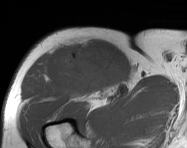
MRI of an extremity soft-tissue mass, one axial slice; position 104 of 114 along the scan axis; MR volume resampled by the dataset authors to the PET/CT grid (not the native acquisition matrix); 3.27 mm slice thickness; 187 × 148 image matrix. Male patient. From the clinical record (not read from this slice): histological type: pleiomorphic leiomyosarcoma; grade: intermediate; site of the primary tumour: right thigh.
Annotated regions visible in this slice (expert contour drawn on MRI and transferred to this co-registered scan by the dataset authors):
- gross tumour volume including surrounding oedema: bounding box <59,40,124,98> (left, top, right, bottom; pixels)
- gross tumour volume (mass): <61,47,122,96>